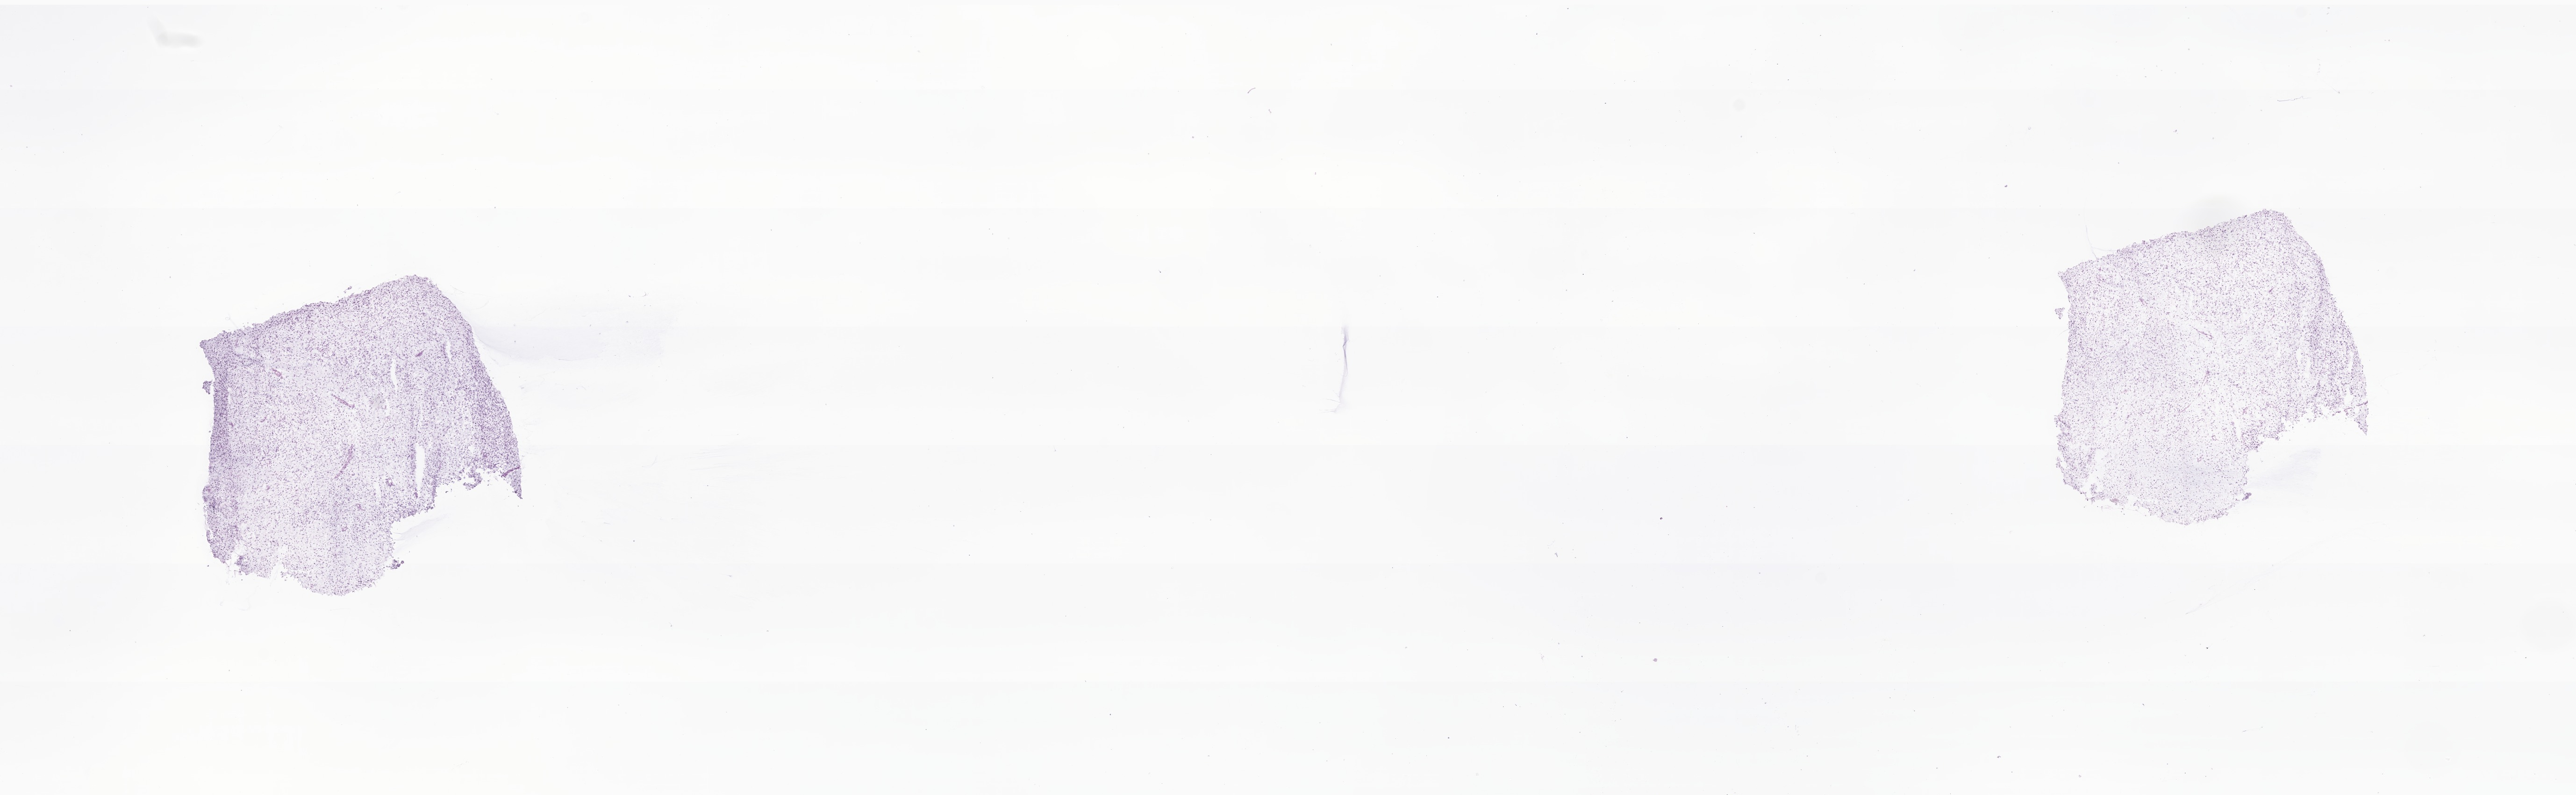
Haematoxylin and eosin whole-slide image of tumor tissue from the testis — low-resolution overview of the scanned area, about 23.2 x 7.2 mm. Frozen section (OCT-embedded). Patient: male, age 197 months (16 years 5 months).
- diagnosis (ICD-O-3 morphology term): Rhabdomyosarcoma, NOS